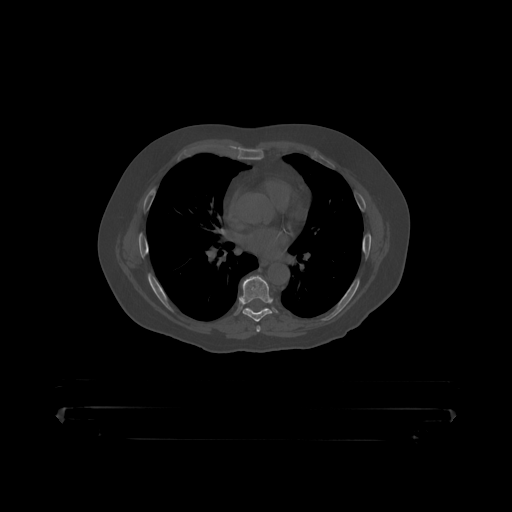
CT including the spine, one axial slice; slice 277 of 390 in the series (ordered by position); reconstruction kernel STANDARD; 120 kVp; bone window (W 1800 / L 400 HU); 1.25 mm slice thickness; 512 × 512 image matrix, field of view 650 × 650 mm. Male patient, age 60 years. From the clinical record (not read from this slice): primary cancer: prostate.
Outlined on this slice (semi-automatic segmentation, software-assisted and operator-edited):
- T7 vertebra: bounding box [x1, y1, x2, y2] px = [241, 276, 272, 319]
- T8 vertebra: [264, 308, 268, 310]